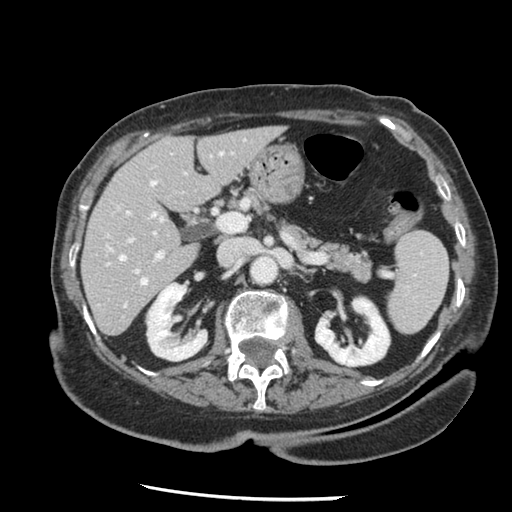
Contrast-enhanced abdominal CT, one axial slice. Slice 71 of 148 in the series (ordered by position). 120 kVp. Intravenous contrast given. Soft-tissue window (W 400 / L 40 HU). 2.5 mm slice thickness. 512 × 512 image matrix, field of view 330 × 330 mm. Female patient, age 85 years. From the clinical record (not read from this slice): diagnosis: colorectal cancer liver metastases, imaged before liver resection; multiple liver metastases: no; largest metastasis: 0.9 cm; chemotherapy before resection: yes.
Structures marked on this image (outlined manually by an expert reader):
- hepatic veins: bounding box (x1, y1, x2, y2) in pixels: (120, 152, 174, 306)
- liver: (83, 127, 282, 335)
- planned liver remnant (the part of the liver to remain after resection): (83, 127, 282, 335)
- portal vein (with intrahepatic branches): (126, 150, 225, 274)